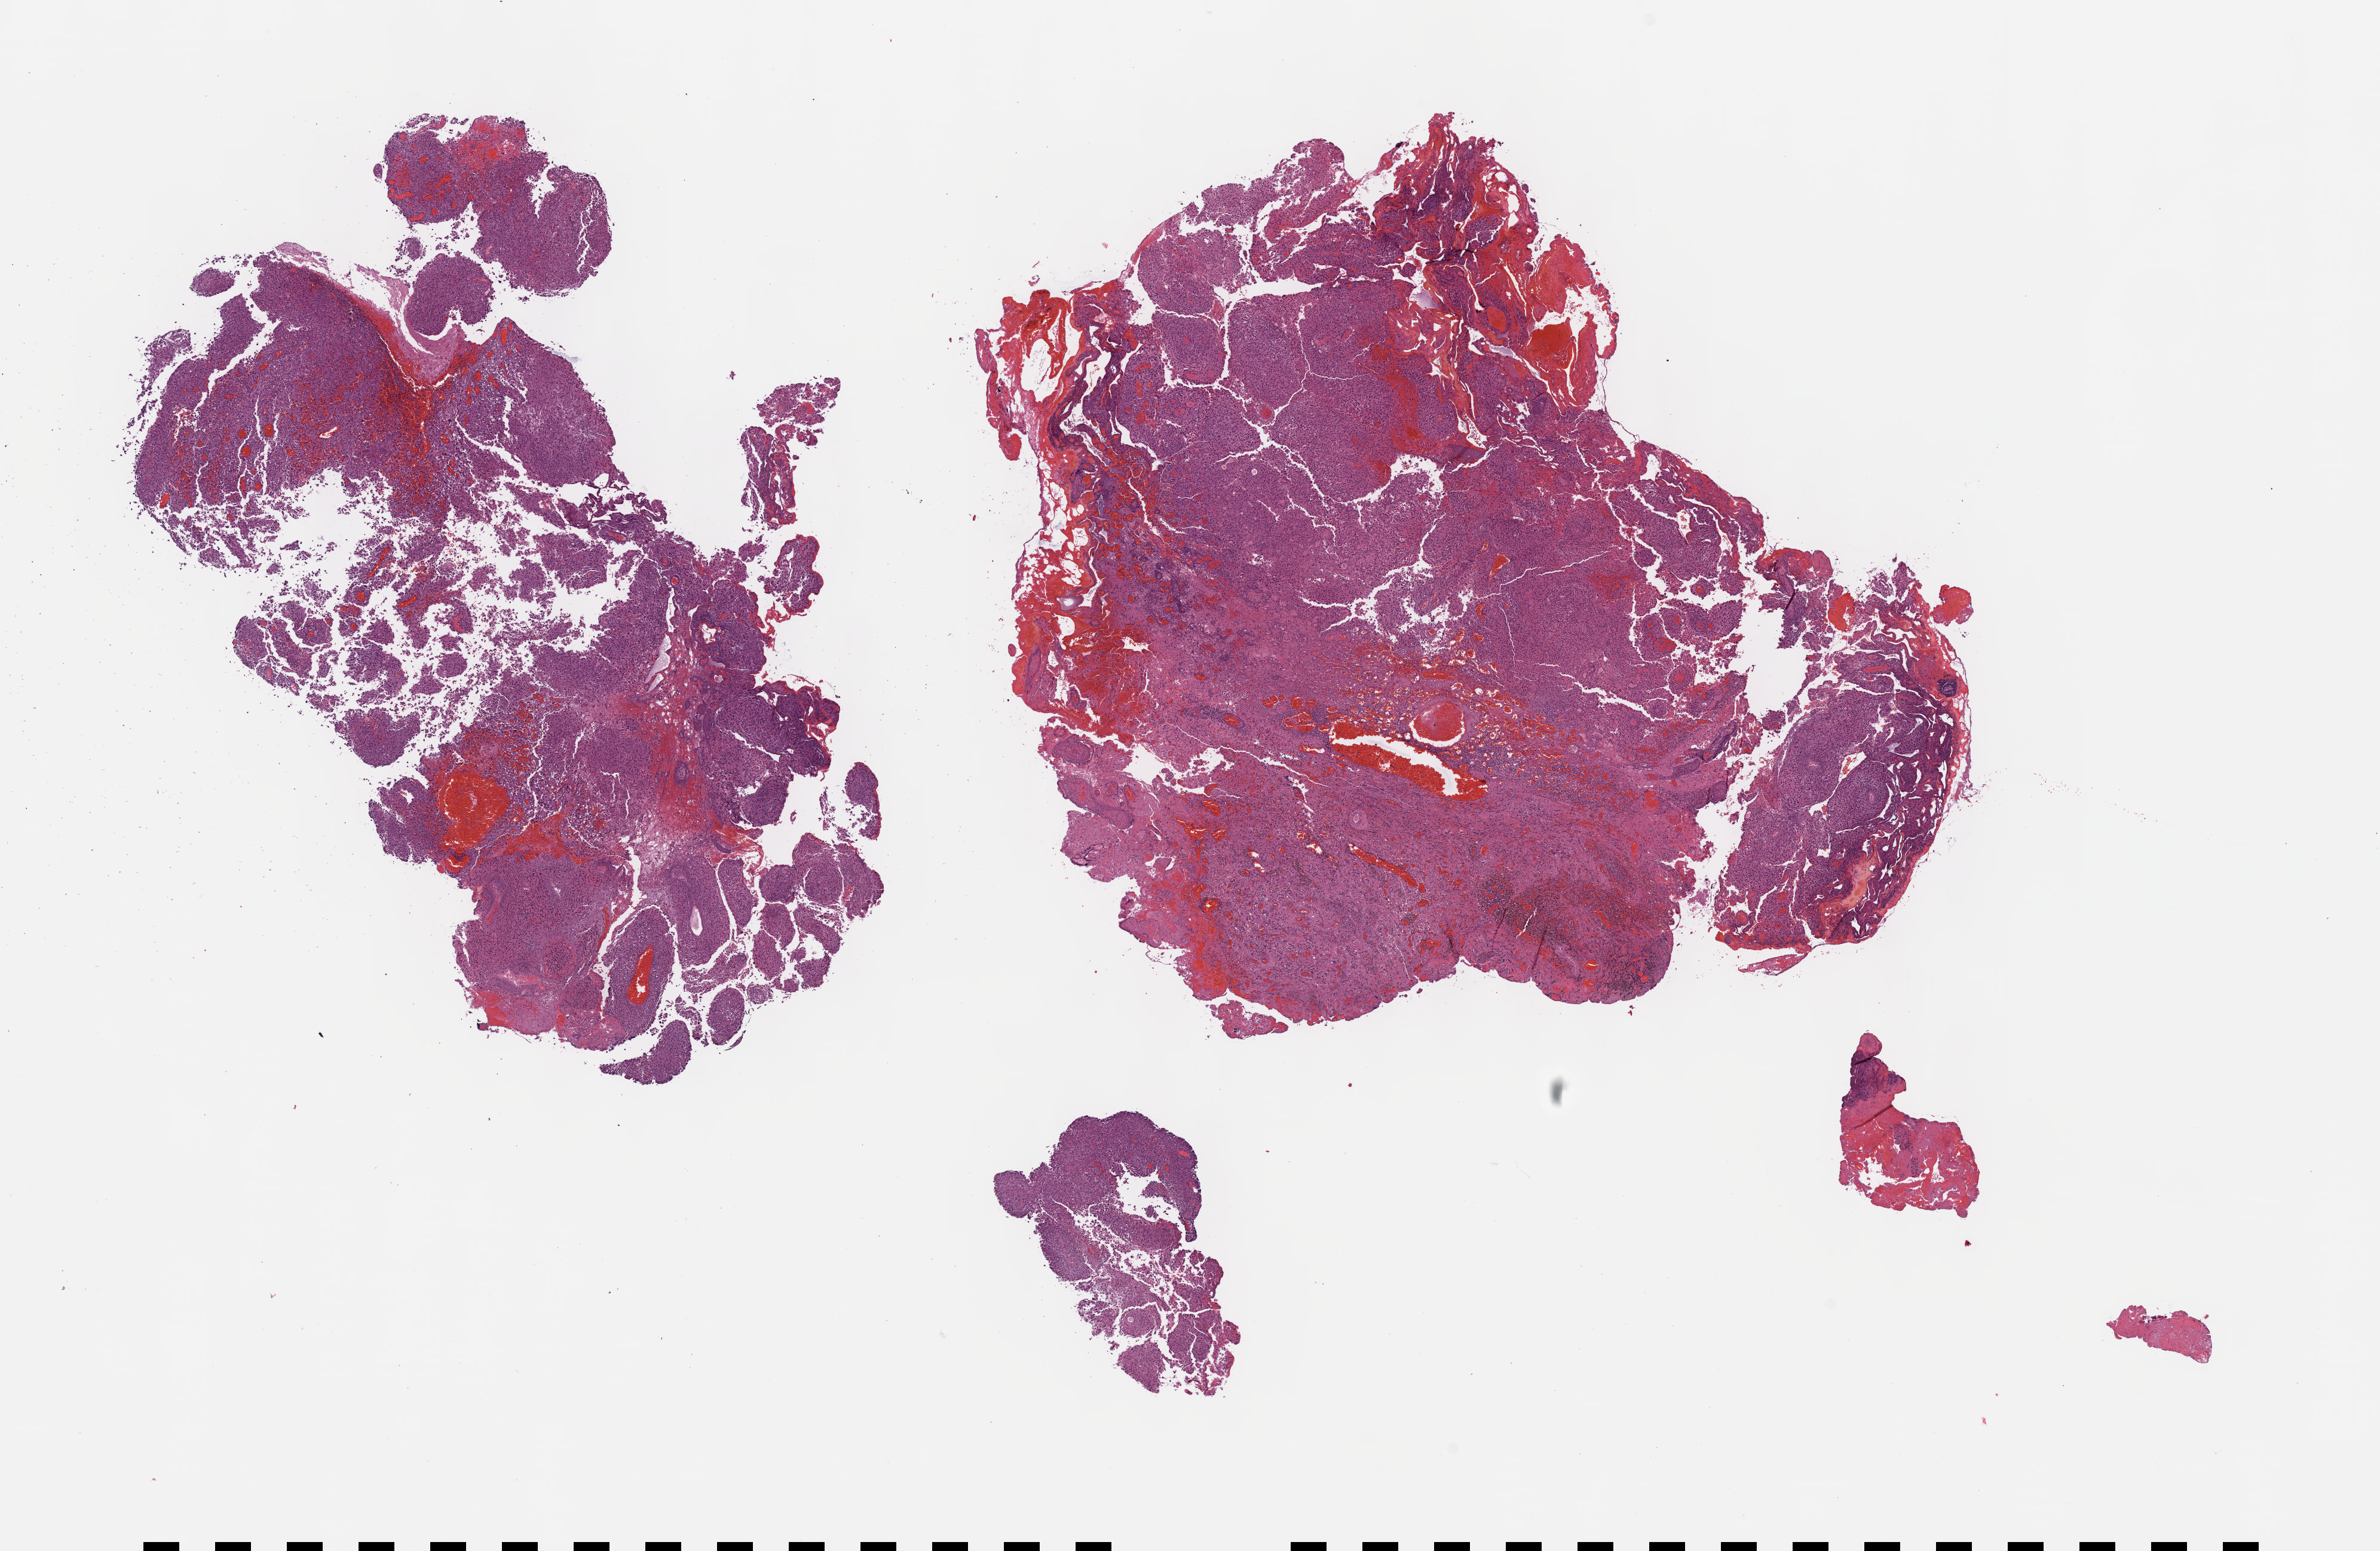
Whole-slide histology image, H&E-stained, whole scanned area (about 16.1 x 10.5 mm) shown as a low-resolution overview; formalin-fixed paraffin-embedded (FFPE) diagnostic section; primary tumour sample from the skin. Male, age 77 years at initial diagnosis.
TNM: TX NX M1c. AJCC pathologic stage: IV. Histologic diagnosis: Malignant melanoma, NOS.